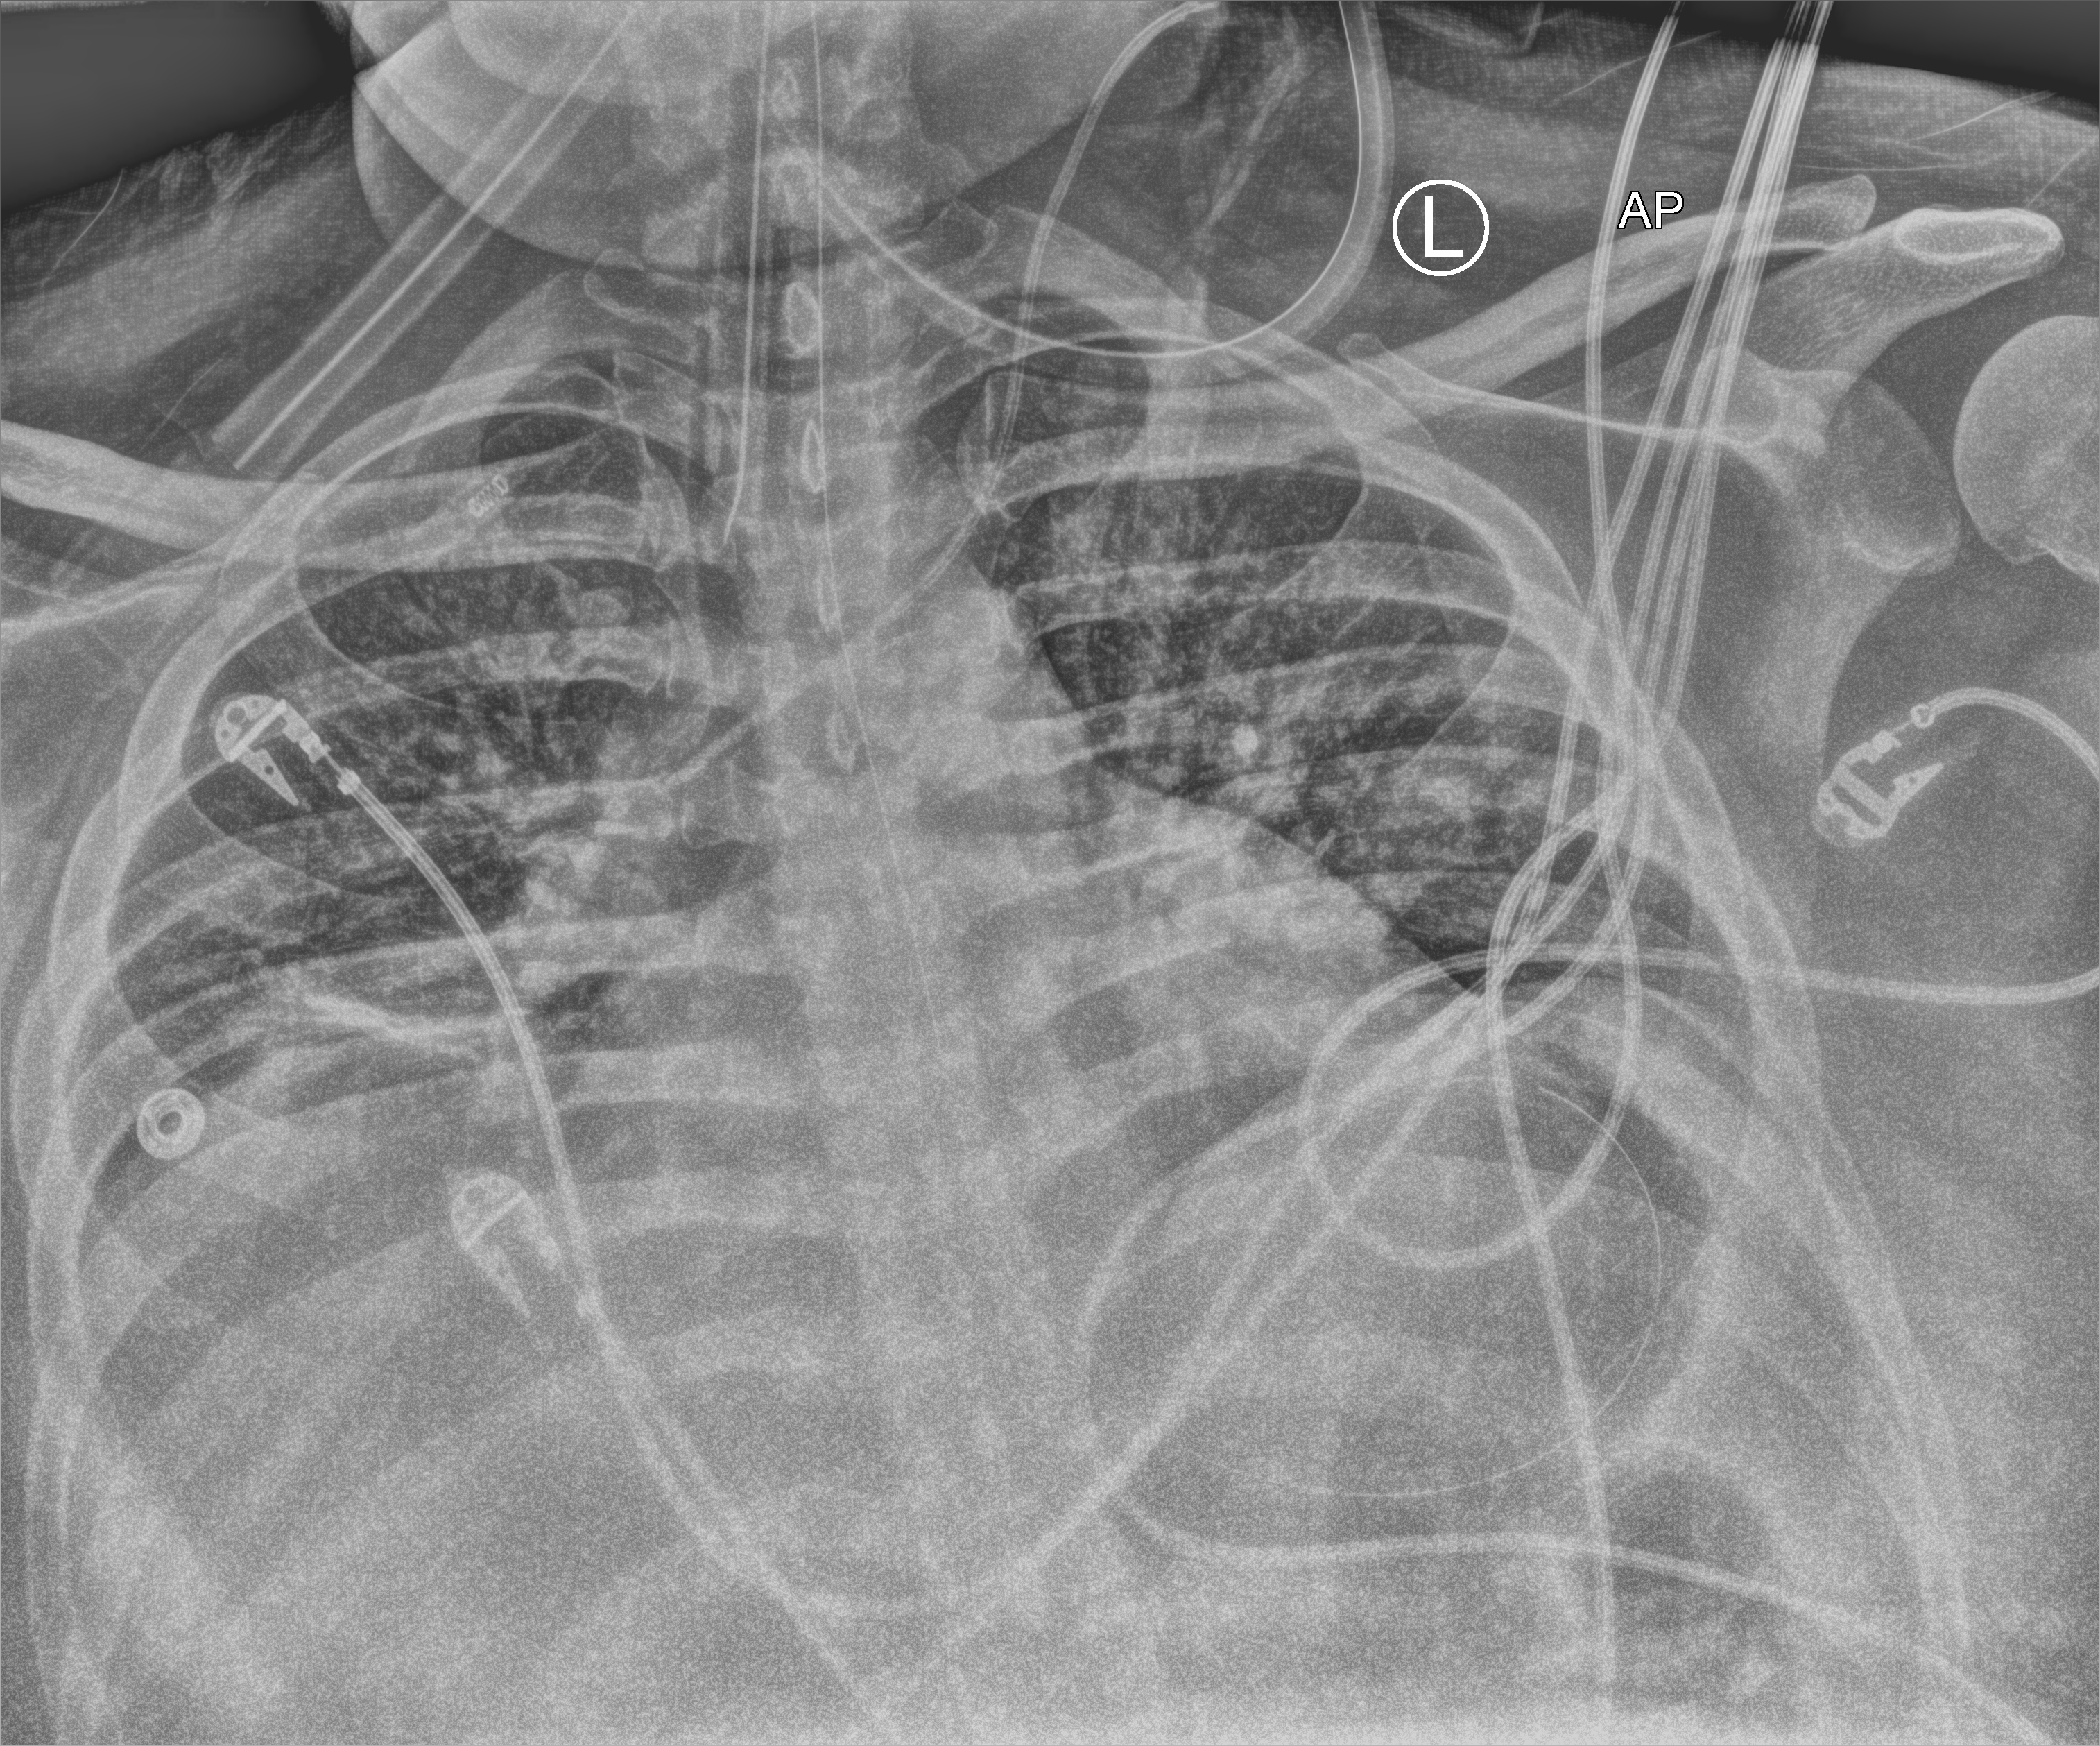
Bedside chest radiograph (computed radiography), anteroposterior (AP) projection. Patient hospitalised with COVID-19; male, aged 18–59 years.
Admission-level facts for this patient (not findings on this image; timing relative to this image not recorded): mechanically ventilated during this hospital stay: yes; admitted to intensive care during this hospital stay: yes.